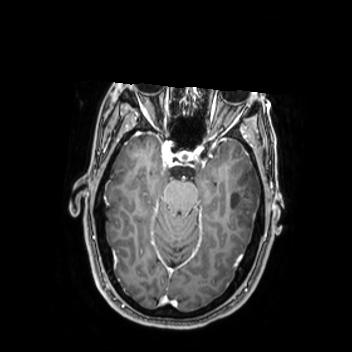
Brain MRI from a brain-tumour surgery series, one axial slice. Position 166 of 350 along the scan axis. T1-weighted post-contrast. 0.9 mm slice thickness. 352 × 352 image matrix, field of view 280 × 280 mm. From the clinical record (not read from this slice): histopathology: Oligodendroglioma; WHO grade: 2; IDH mutation: yes; tumour location: Left Middle Temporal Gyrus.
Outlined on this slice (expert manual segmentation):
- tumour: bounding box [x1, y1, x2, y2] px = [224, 163, 262, 226]